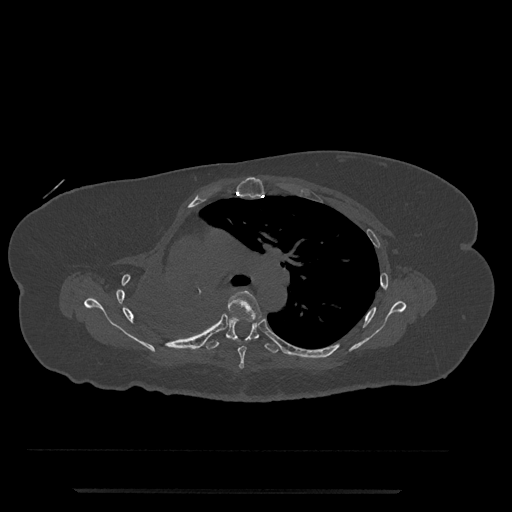
CT including the spine, one axial slice. Slice 518 of 797 in the series (ordered by position). 120 kVp. Bone window (W 1800 / L 400 HU). 0.5 mm slice thickness. 512 × 512 image matrix. Female patient, age 51 years. Case-level facts recorded for this patient, not image findings: primary cancer: neuro.
Structures marked on this image (semi-automatic segmentation, software-assisted and operator-edited):
- T5 vertebra: bounding box <196,290,263,369> (left, top, right, bottom; pixels)
- T6 vertebra: <206,318,278,353>